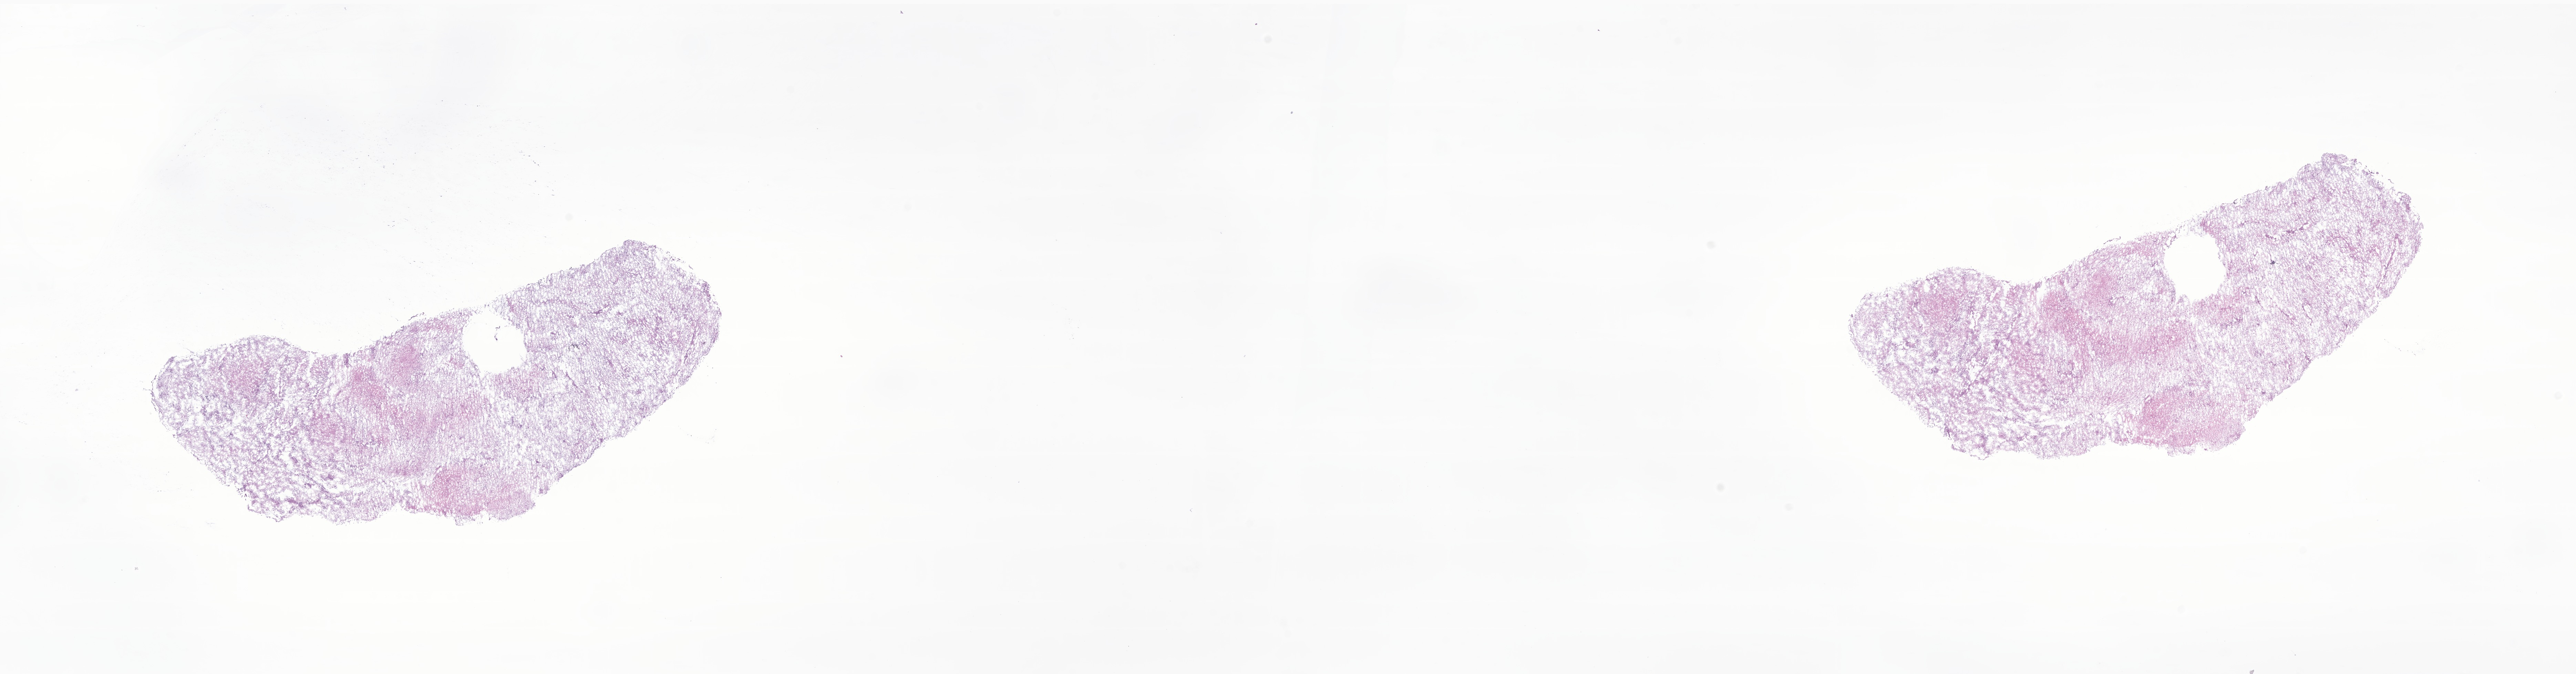
Digitized H&E-stained section of tumor tissue from the cerebellum — a low-resolution overview of the entire scanned area, about 31.5 x 8.2 mm; cryosection (OCT / tissue freezing medium). Patient female; age 40 months (3 years 4 months).
Diagnosis (ICD-O-3 morphology term): Pilocytic astrocytoma.